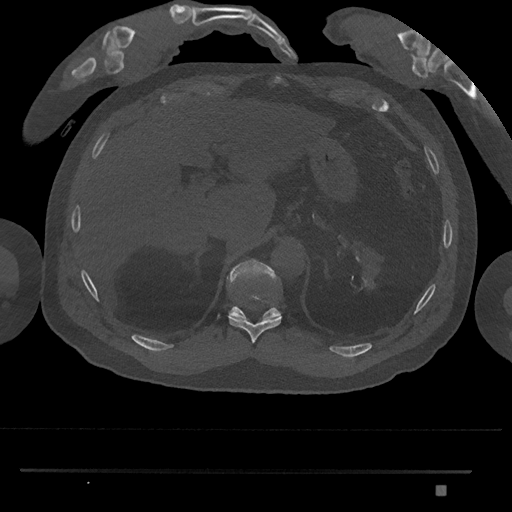
CT including the spine, one axial slice; position 982 of 1134 along the scan axis; reconstruction kernel Br40s/3; 120 kVp; bone window (W 1800 / L 400 HU); 0.5 mm slice thickness; 512 × 512 image matrix. Male patient, age 65 years. From the clinical record (not read from this slice): primary cancer: prostate.
Annotated regions visible in this slice (semi-automatically segmented with operator editing):
- T10 vertebra: bounding box (x1, y1, x2, y2) in pixels: (228, 295, 282, 343)
- T11 vertebra: (226, 259, 281, 321)